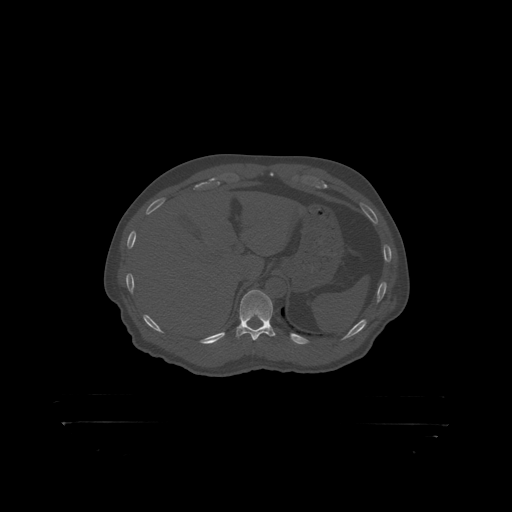
CT including the spine, one axial slice. Slice 378 of 399 in the series (ordered by position). 120 kVp. Bone window (W 1800 / L 400 HU). 1.25 mm slice thickness. 512 × 512 image matrix, field of view 650 × 650 mm. Patient: male, 46 years. From the clinical record (not read from this slice): primary cancer: skin.
Annotated regions visible in this slice (semi-automatic segmentation, software-assisted and operator-edited):
- T11 vertebra: bounding box <240,290,273,319> (left, top, right, bottom; pixels)